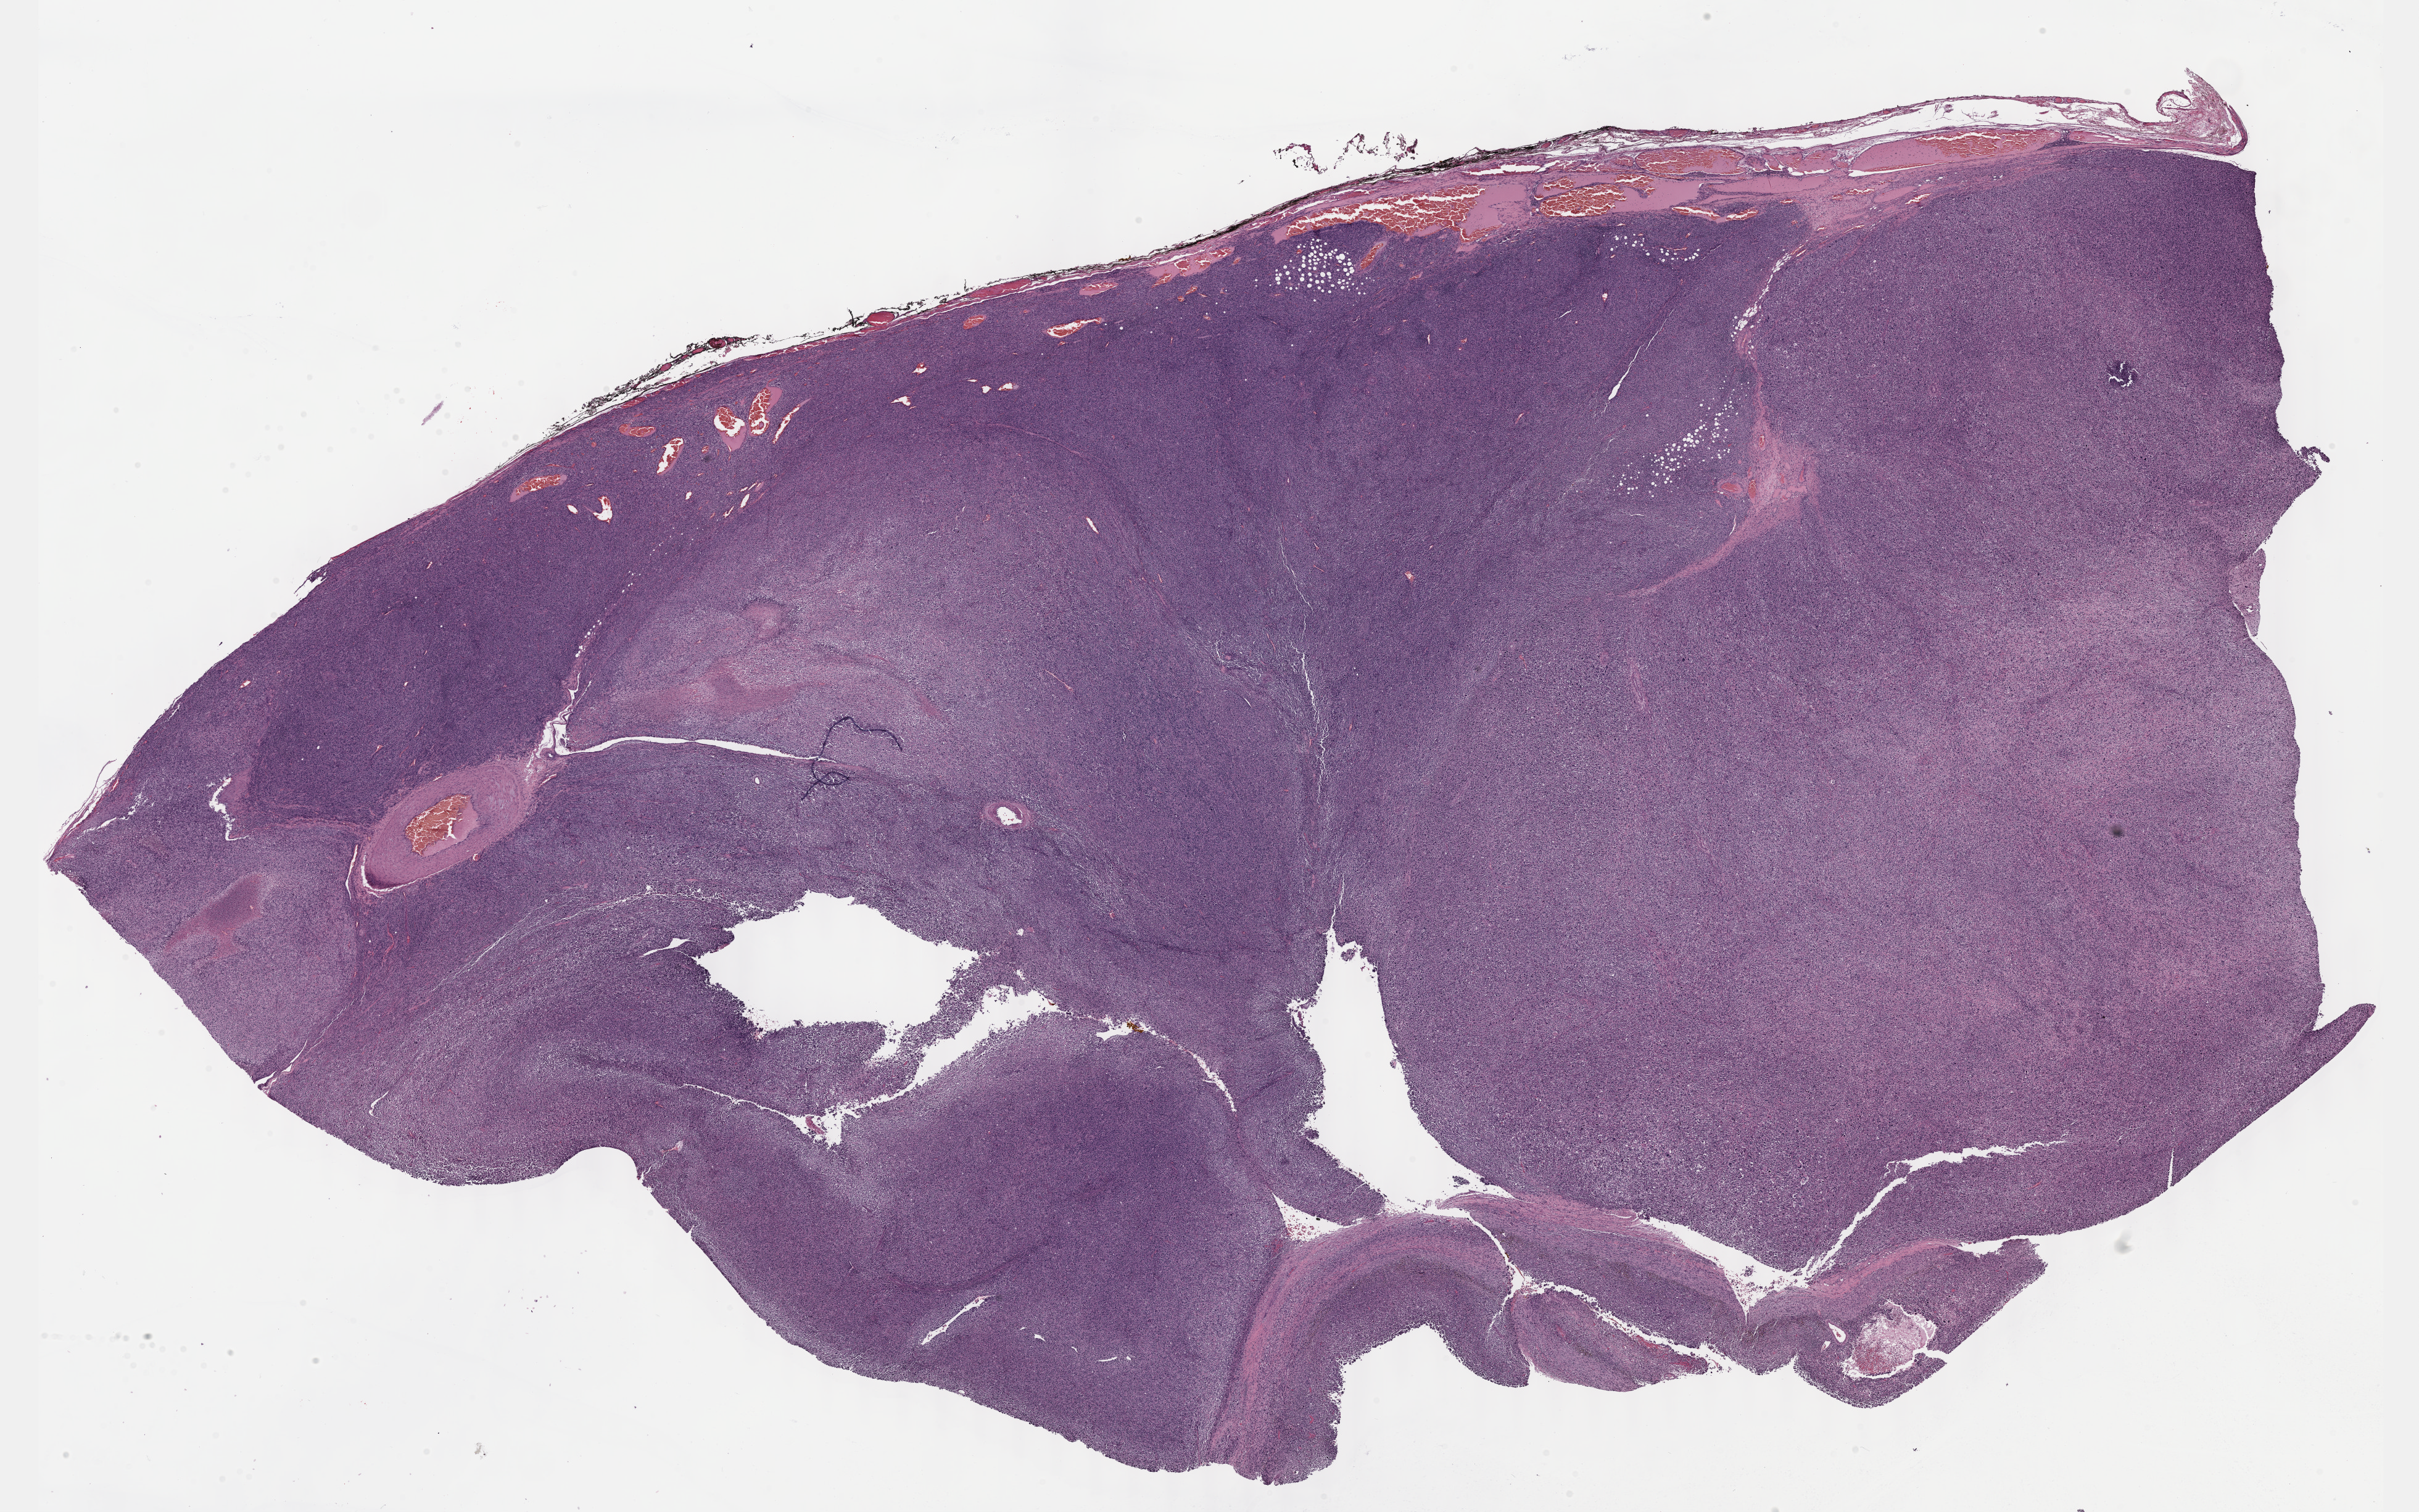
Whole-slide histology image, H&E — a low-resolution overview of the entire scanned area, about 31.7 x 19.8 mm; formalin-fixed paraffin-embedded (FFPE) diagnostic section; connective, subcutaneous and other soft tissues, primary tumour sample. Patient: male, age at initial diagnosis 29 years.
- diagnosis: Malignant peripheral nerve sheath tumor (connective, subcutaneous and other soft tissues of lower limb and hip)